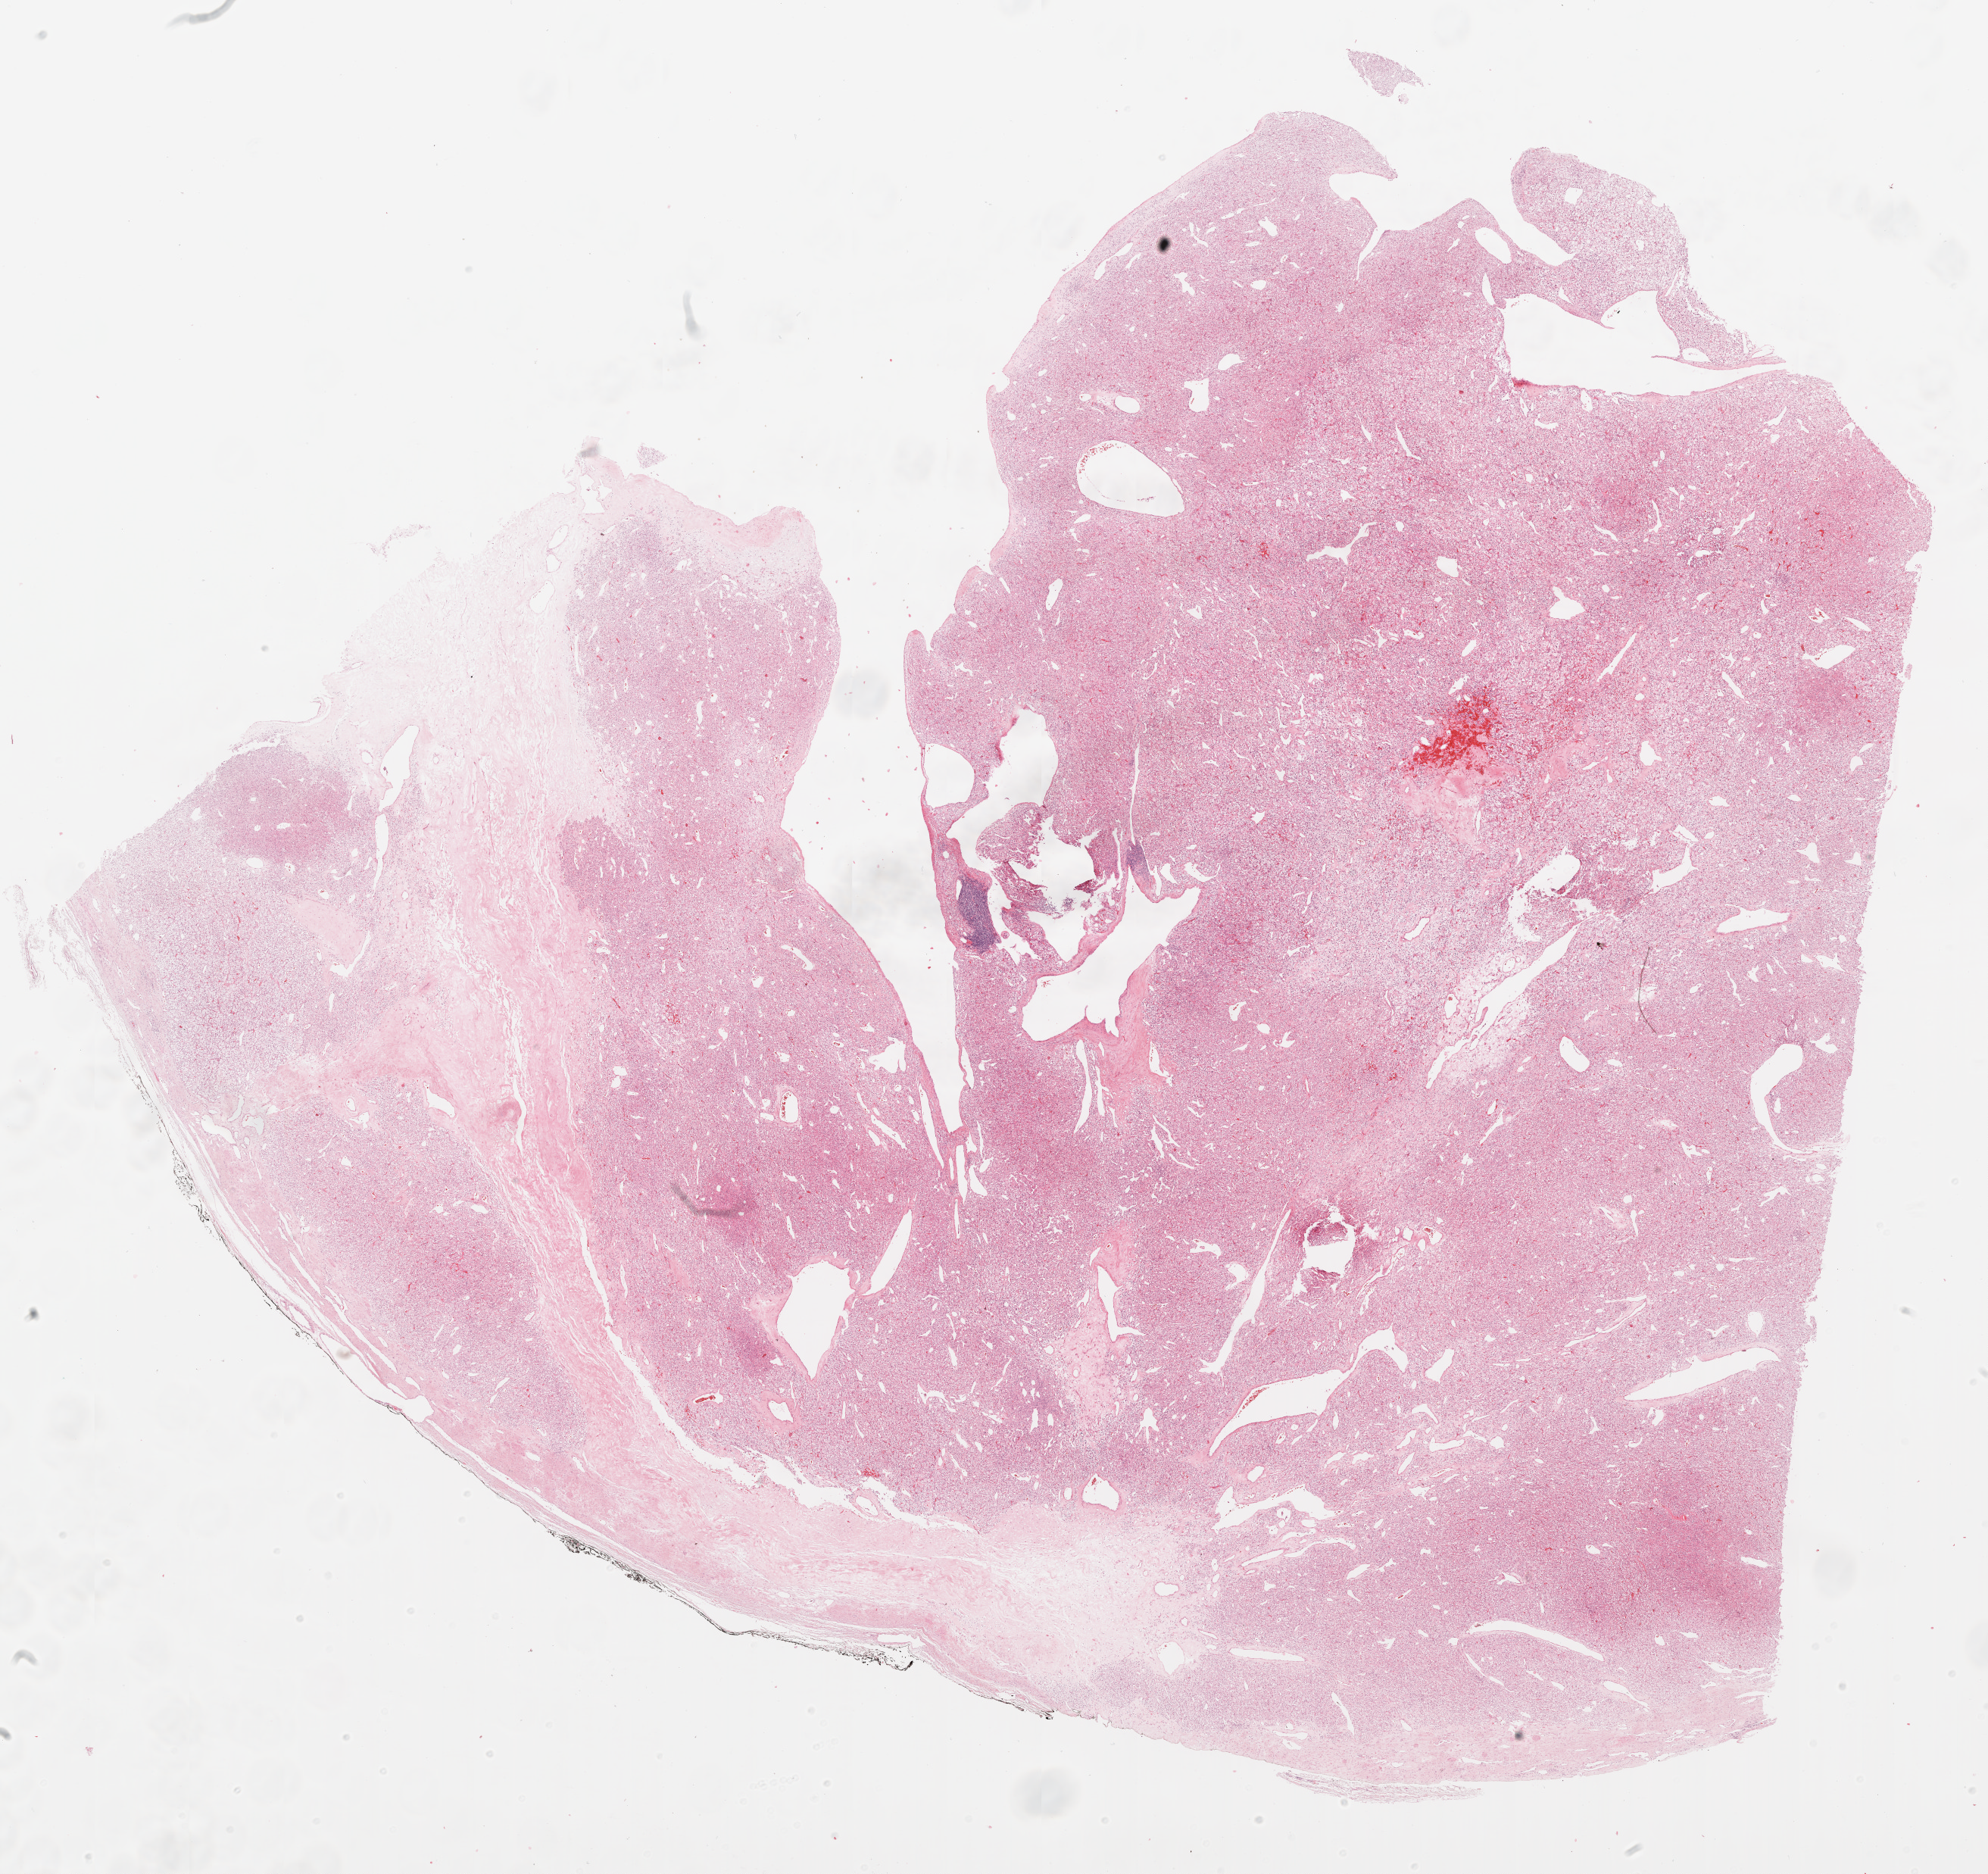
H&E-stained whole-slide image — a low-resolution overview of the entire scanned area, about 21.1 x 19.9 mm; formalin-fixed paraffin-embedded (FFPE) diagnostic section; sample: primary tumour, kidney. Male patient; age at initial diagnosis 82 years. Histologic grade: G2 (moderately differentiated).
• AJCC pathologic stage: I
• histologic diagnosis: Clear cell adenocarcinoma, NOS
• TNM: T1a NX M0
• laterality: right